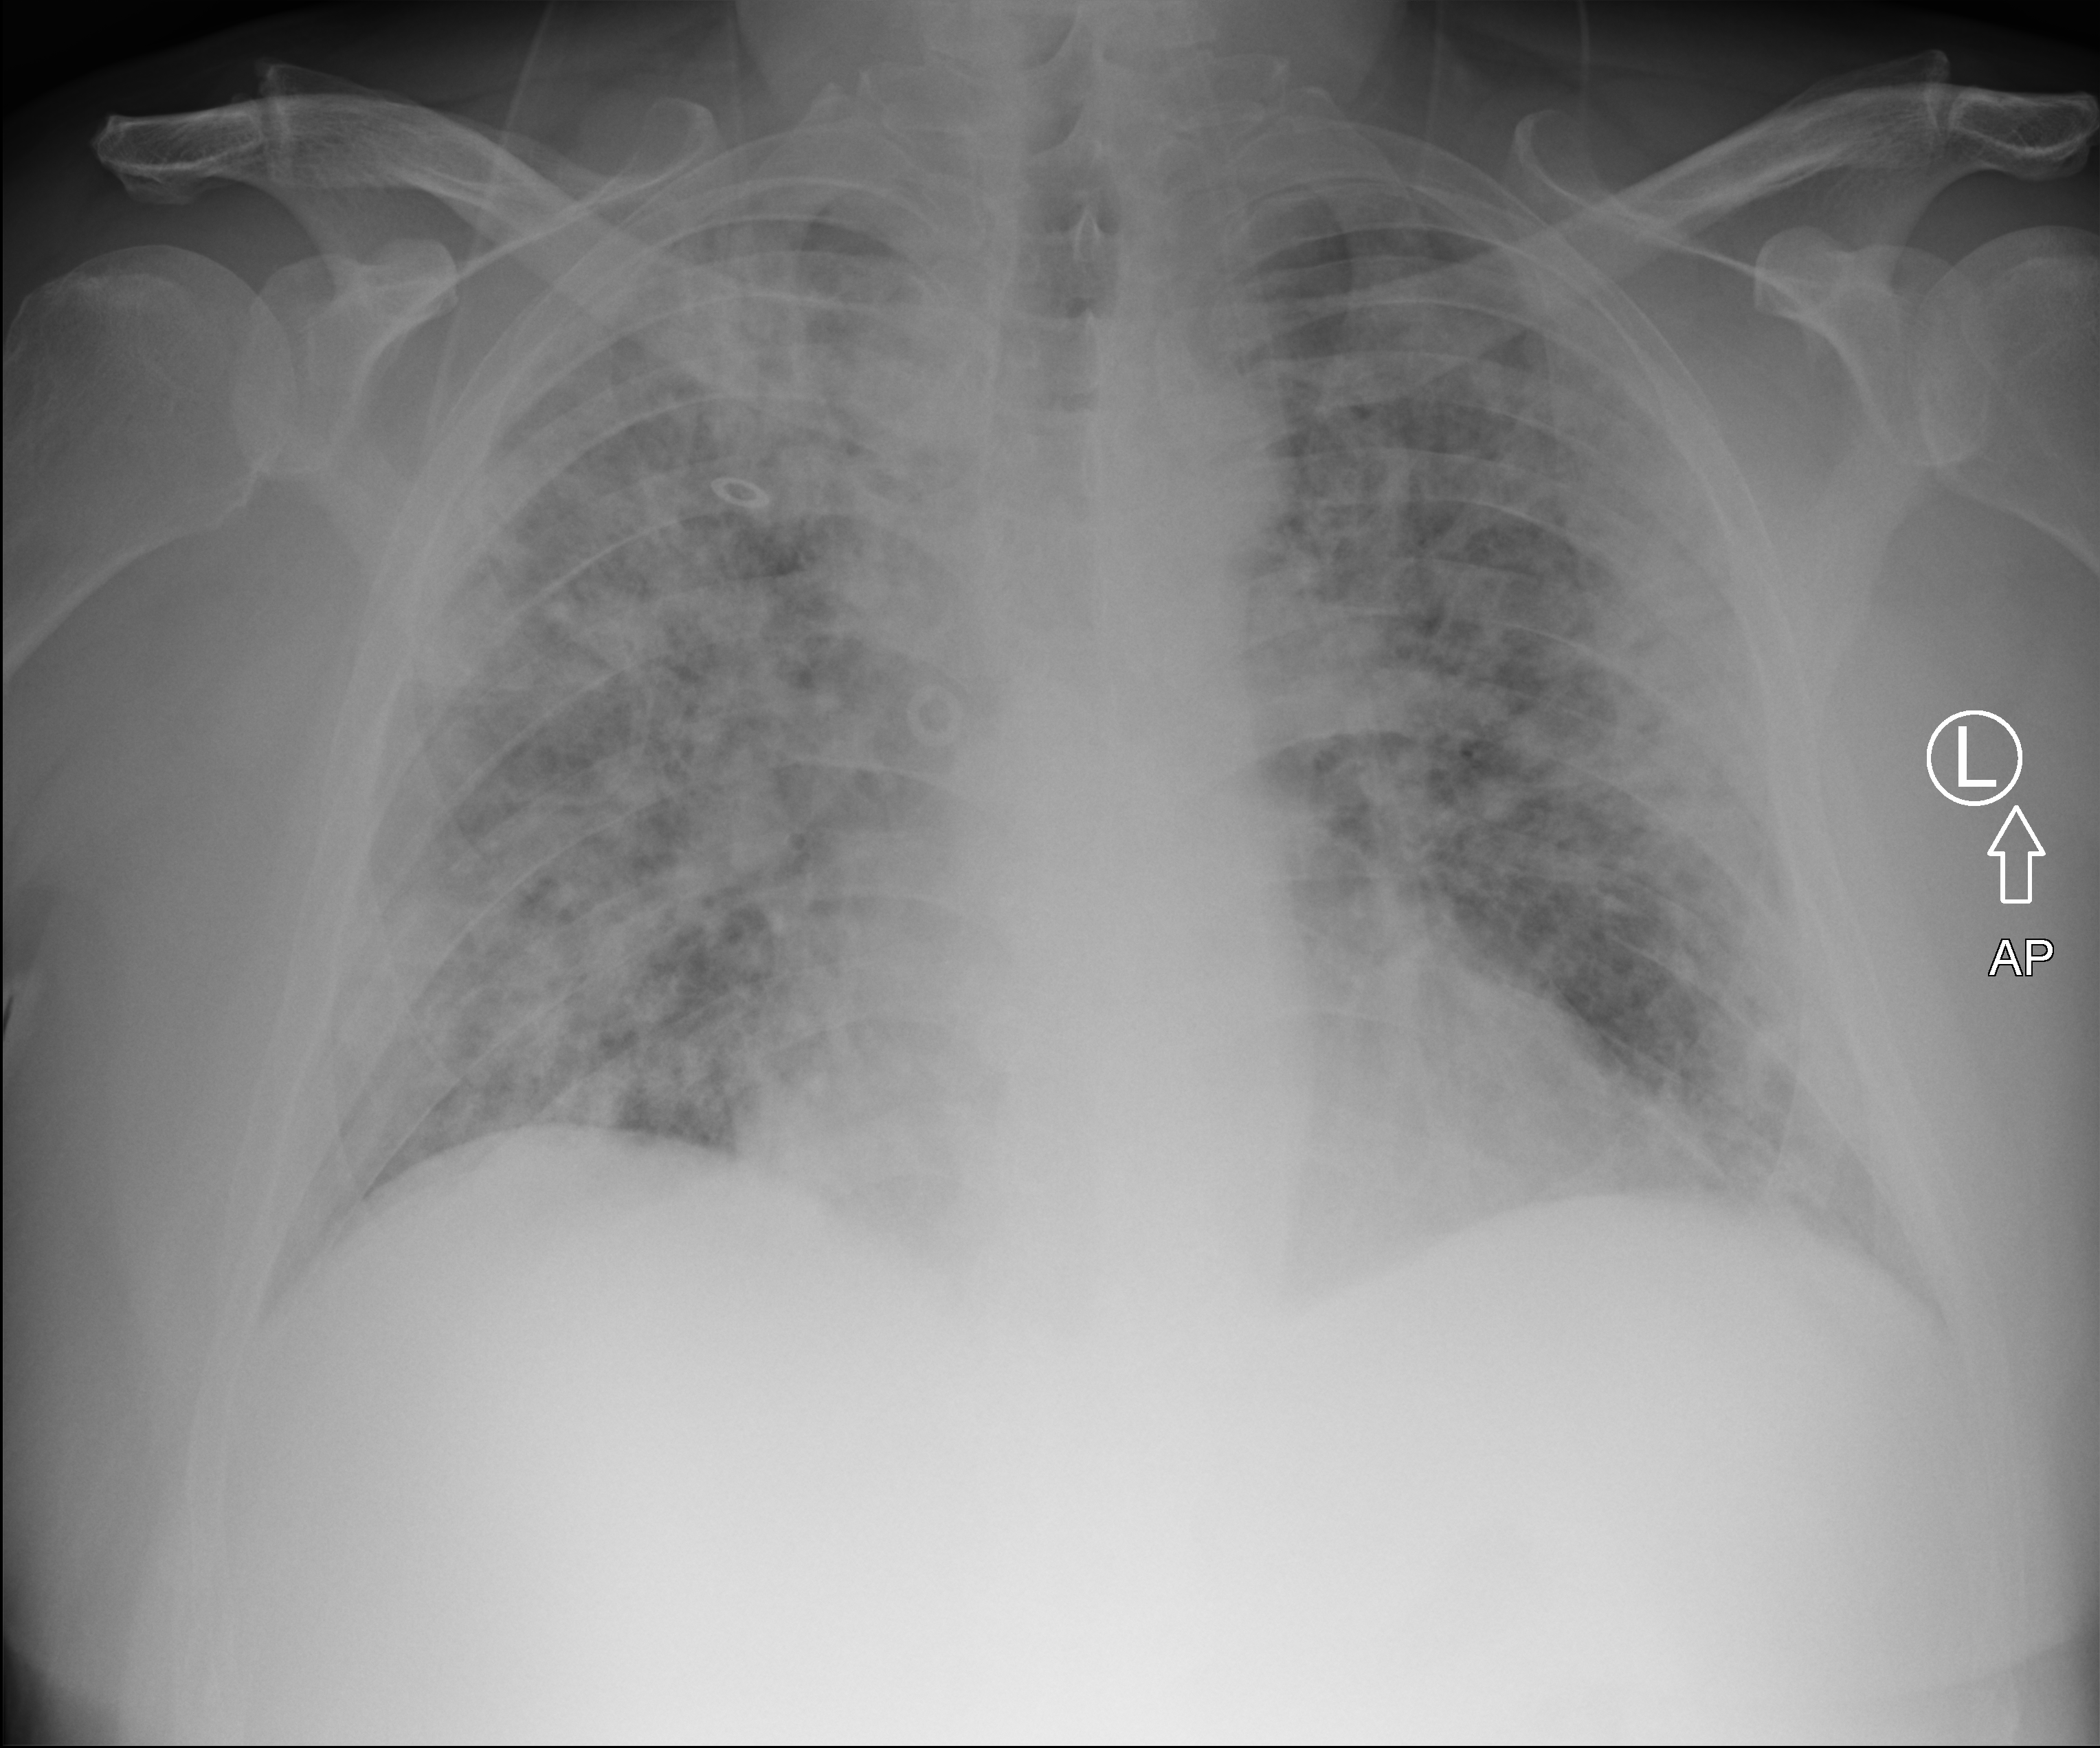
Chest radiograph; anteroposterior (AP) projection. Patient hospitalised with COVID-19; male, aged 60–74 years.
Hospital-stay facts (about this admission, not read from this image; timing relative to this image not recorded): admitted to intensive care during this hospital stay: no; mechanically ventilated during this hospital stay: no; length of hospital stay: 9 days.